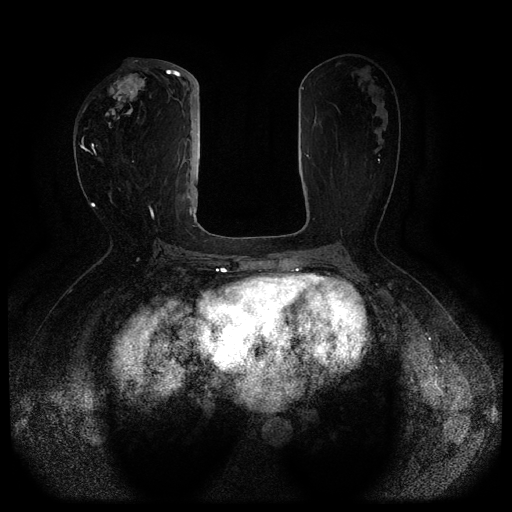
Breast MRI (dynamic contrast-enhanced, multi-phase), one axial slice; slice 42 of 116 in the series (ordered by position); dynamic contrast-enhanced series, time point 2 of 5 at this slice position (early post-contrast); 1.5 T; TE 2.6 ms, TR 5.3 ms; 512 × 512 image matrix, field of view 350 × 350 mm. Female patient, age 51 years.
Outlined on this slice (semi-automatic segmentation, software-assisted and operator-edited):
- breast lesion (labelled 'tumour' in the annotation; benign lesions carry a separate 'benign' label): bounding box (x1, y1, x2, y2) in pixels: (105, 73, 151, 128)